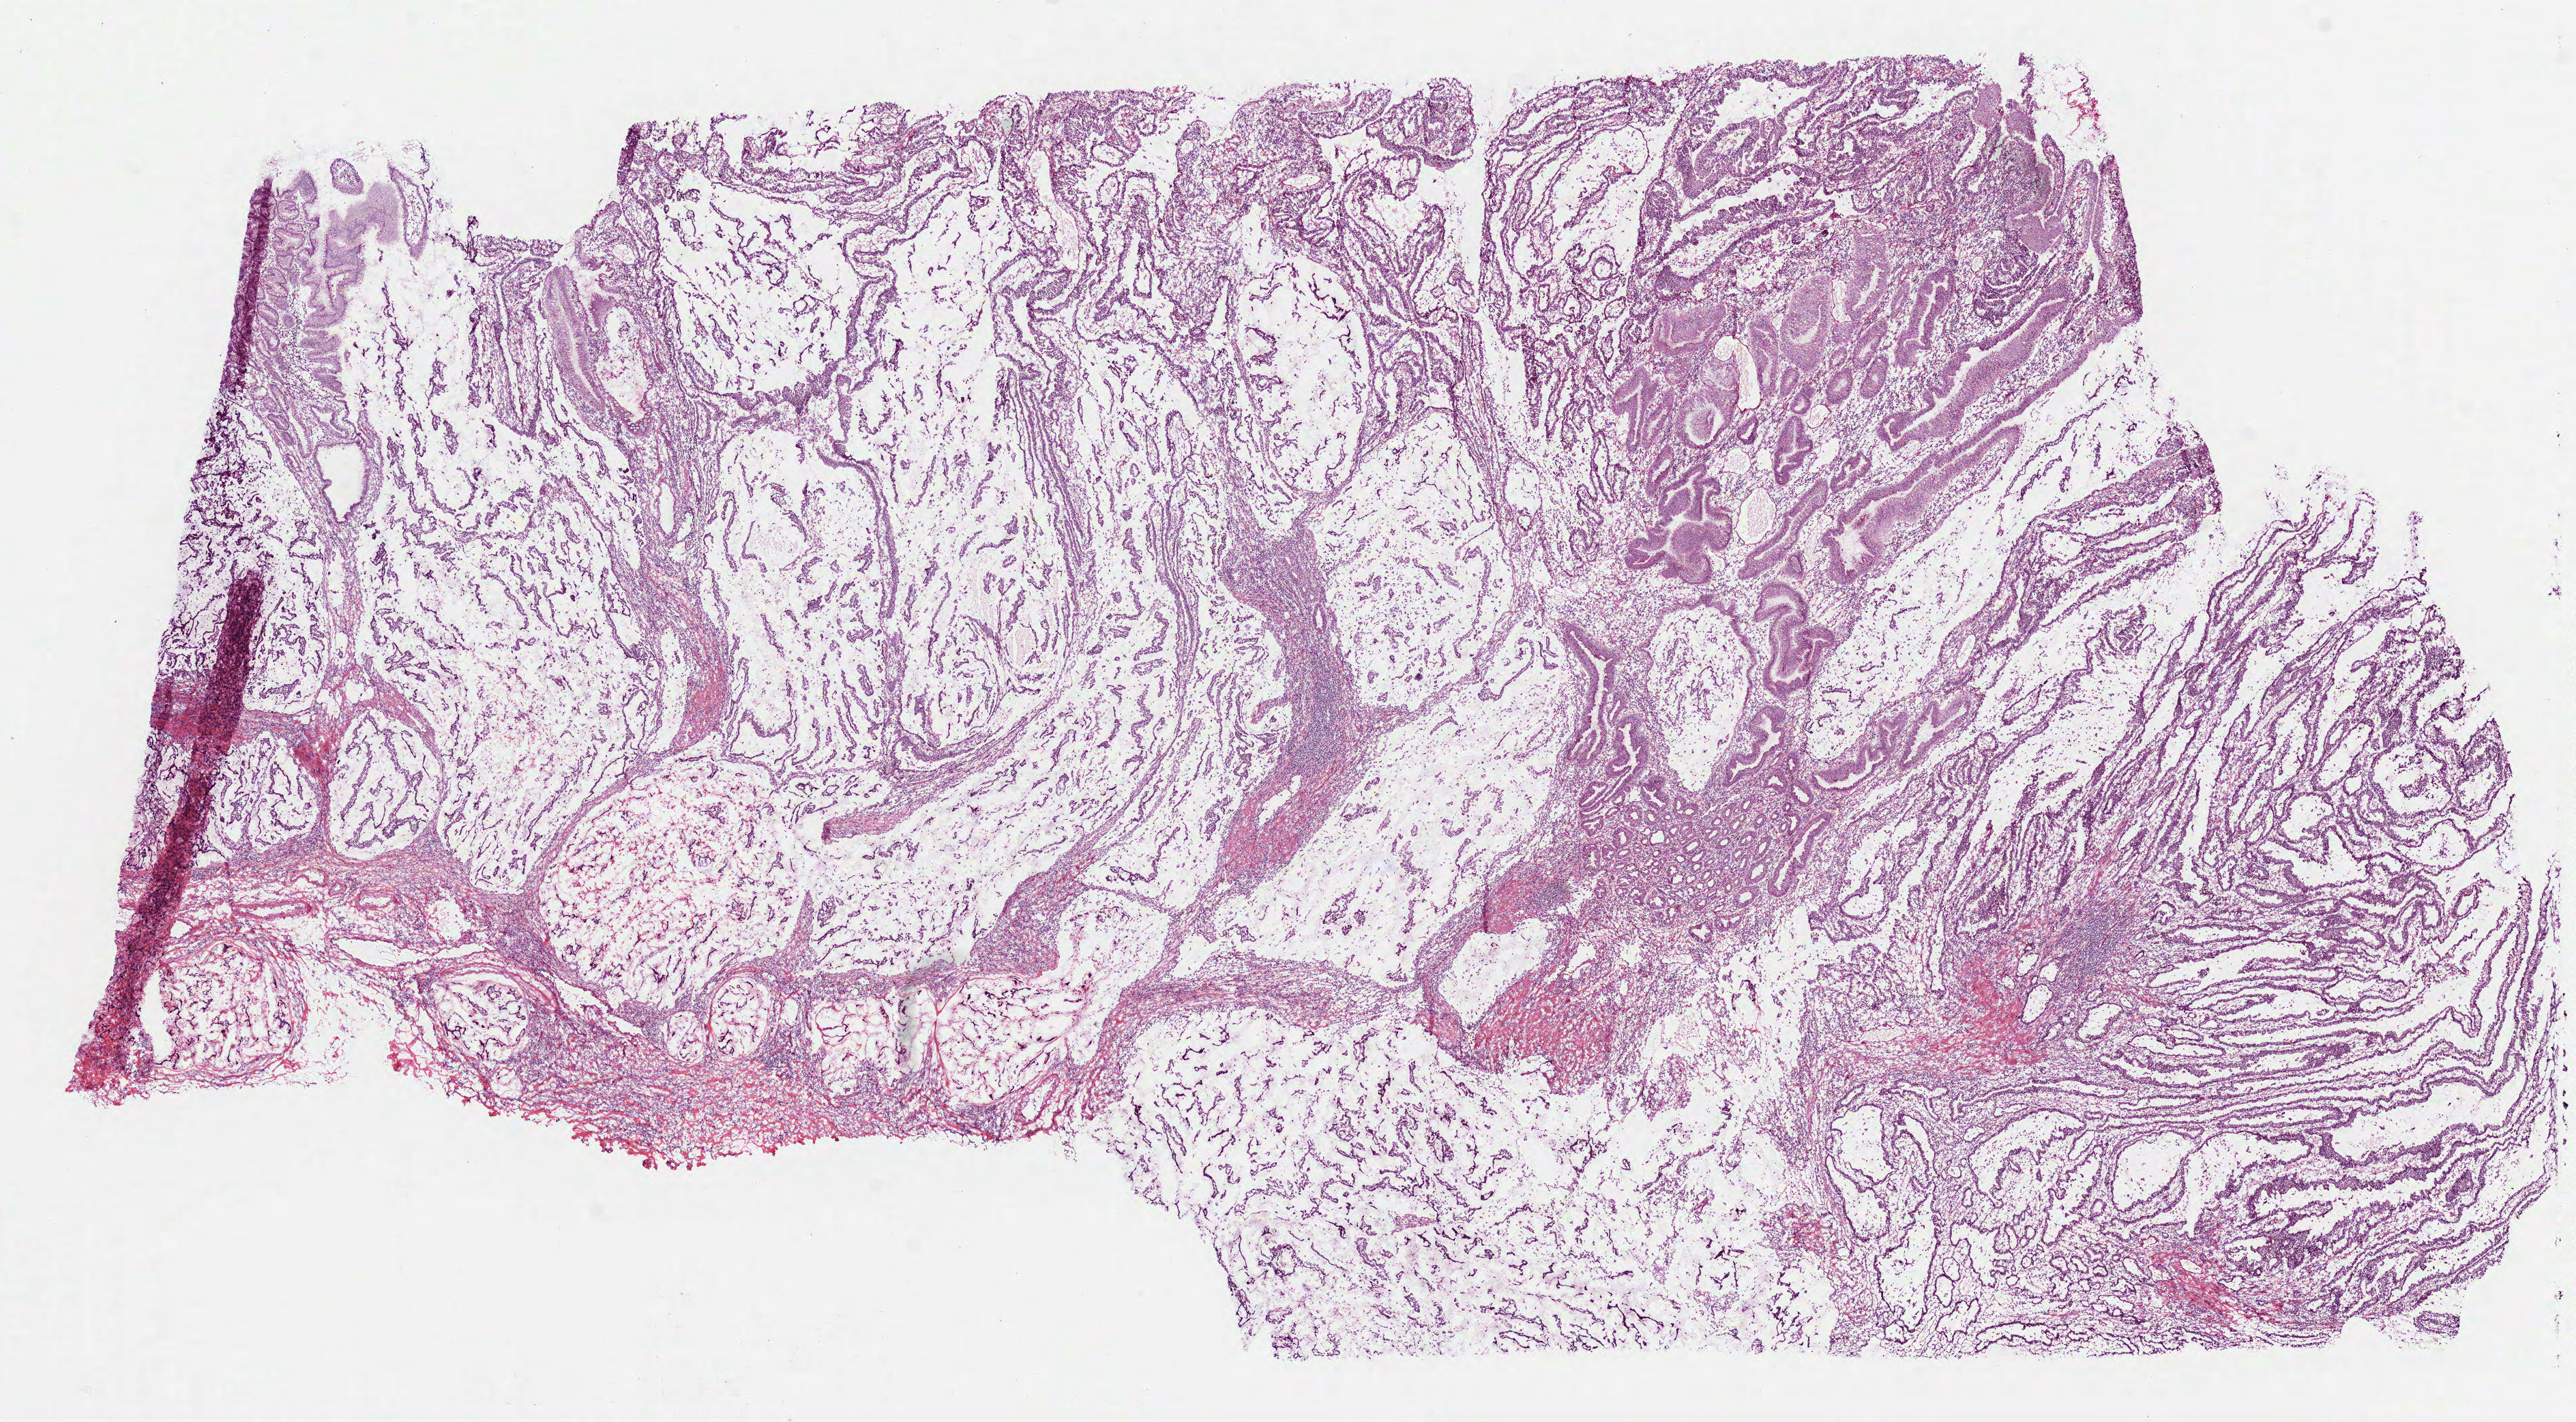
Whole-slide histology image, Hematoxylin and eosin (H&E) stained — a low-resolution overview of the entire scanned area, about 15.2 x 8.4 mm (from a 40x scan), frozen section from the bottom of the tissue portion, sample: primary tumour, stomach. Patient sex: female. Histologic grade: G2 (moderately differentiated). Slide review estimates, as recorded: tumour cells 99%, tumour nuclei 60%, normal cells 1%, stromal cells 0%, necrosis 0%. Infiltration values recorded for this section: lymphocyte infiltration 20%, monocyte infiltration 0%, neutrophil infiltration 15%.
AJCC pathologic stage: IV. Diagnosis: Mucinous adenocarcinoma.